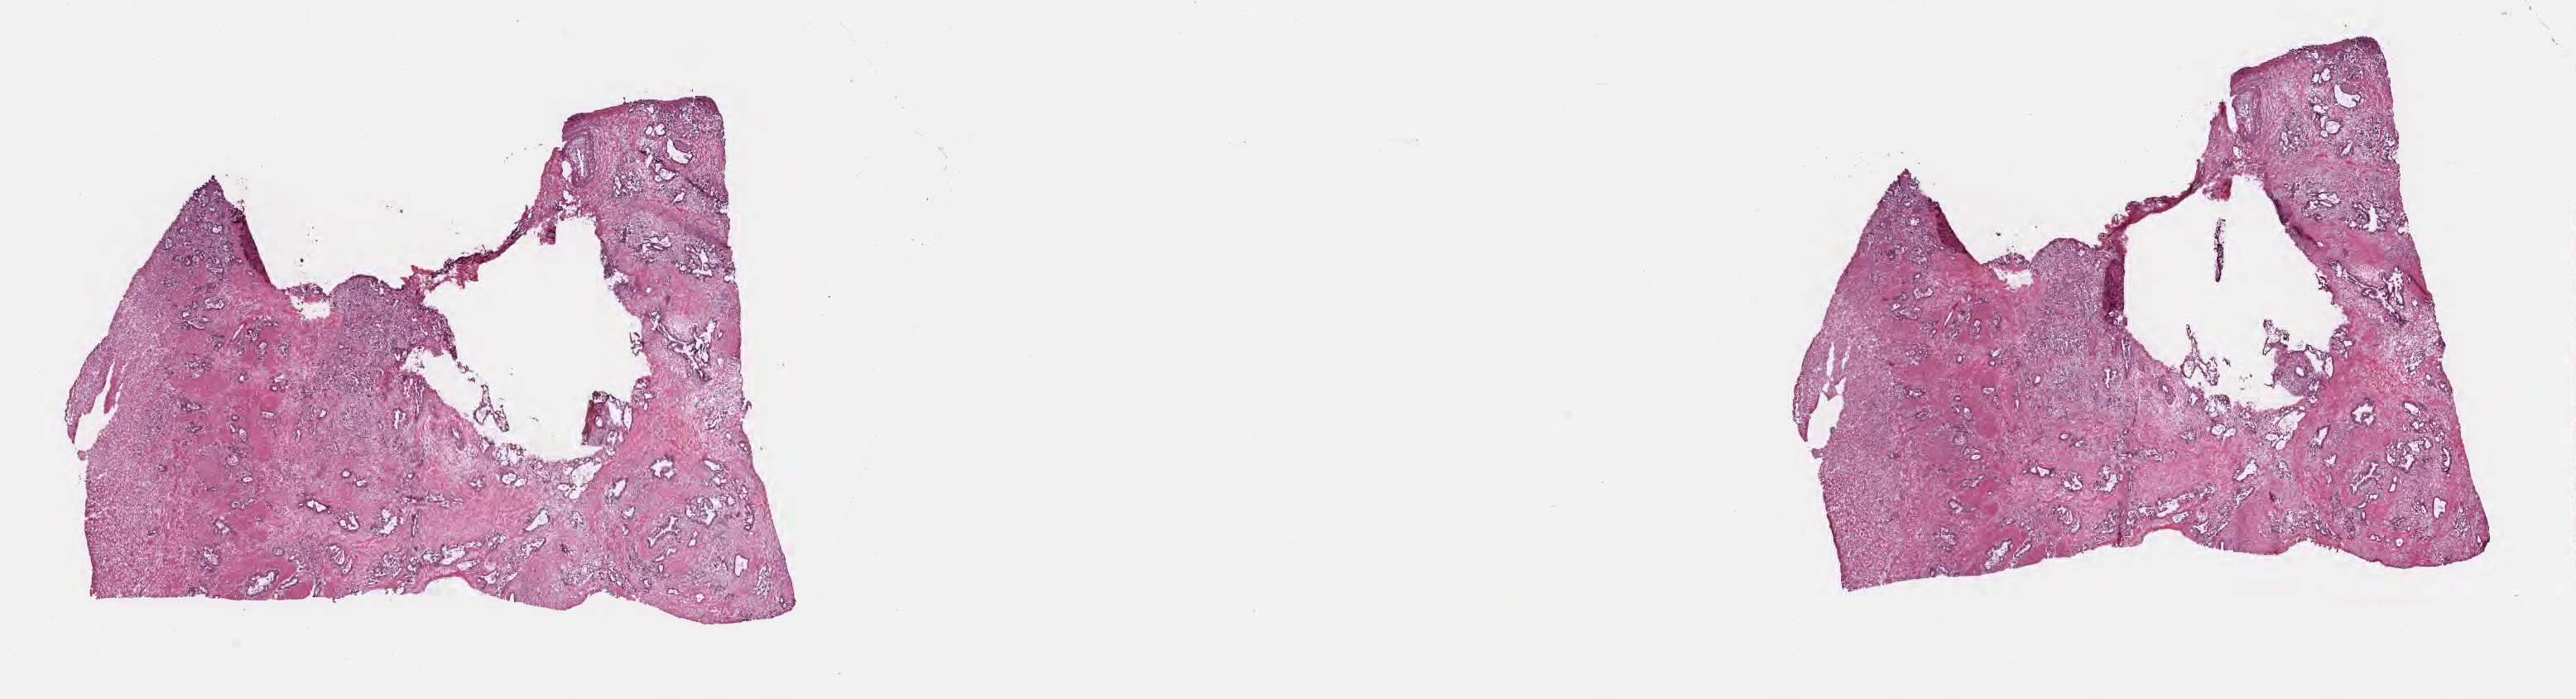
Digitized haematoxylin and eosin-stained section — low-resolution overview of the scanned area, about 25.2 x 6.8 mm; cryosection; specimen: primary tumor; site: head of pancreas. Male patient; age at initial diagnosis 67 years. Slide review estimates, as recorded: tumor cells 75%, tumor nuclei 75%.
Diagnosis: Infiltrating duct carcinoma, NOS.